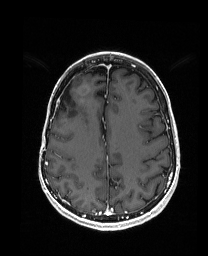
Brain MRI from a brain-tumour surgery series, one axial slice; position 63 of 192 along the scan axis; T1-weighted post-contrast; 1 mm slice thickness; 208 × 256 image matrix, field of view 203 × 250 mm. Case-level facts recorded for this patient, not image findings: histopathology: Metastatic Carcinoma from Breast primary.
Structures marked on this image (expert manual segmentation):
- previous resection cavity: box from (x=55, y=84) to (x=72, y=115) px
- tumour: (x=77, y=85)–(x=89, y=94)